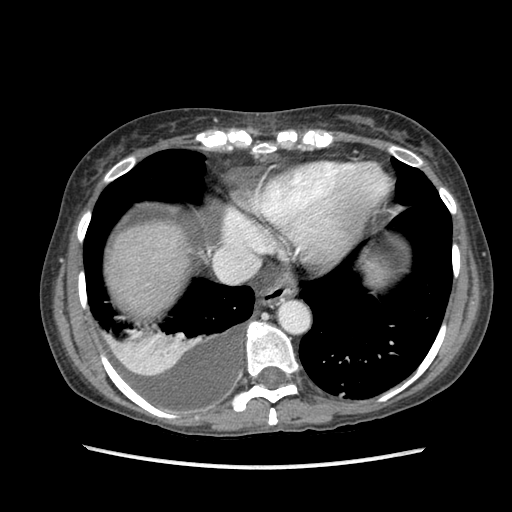
Contrast-enhanced abdominal CT (liver protocol), one axial slice; position 80 of 87 along the scan axis; reconstruction kernel STANDARD; 120 kVp; soft-tissue window (W 400 / L 40 HU); 512 × 512 image matrix, field of view 340 × 340 mm. Case-level facts recorded for this patient, not image findings: diagnosis: hepatocellular carcinoma (patient treated with transarterial chemoembolisation; whether this scan precedes or follows treatment is not stated here); TNM stage (as recorded): Stage-IIIB.
Outlined on this slice (semi-automatic segmentation, software-assisted and operator-edited):
- liver parenchyma outside the tumour (the mass and vessels are separate outlines, so this box may not span the whole liver): box from (x=108, y=222) to (x=186, y=309) px